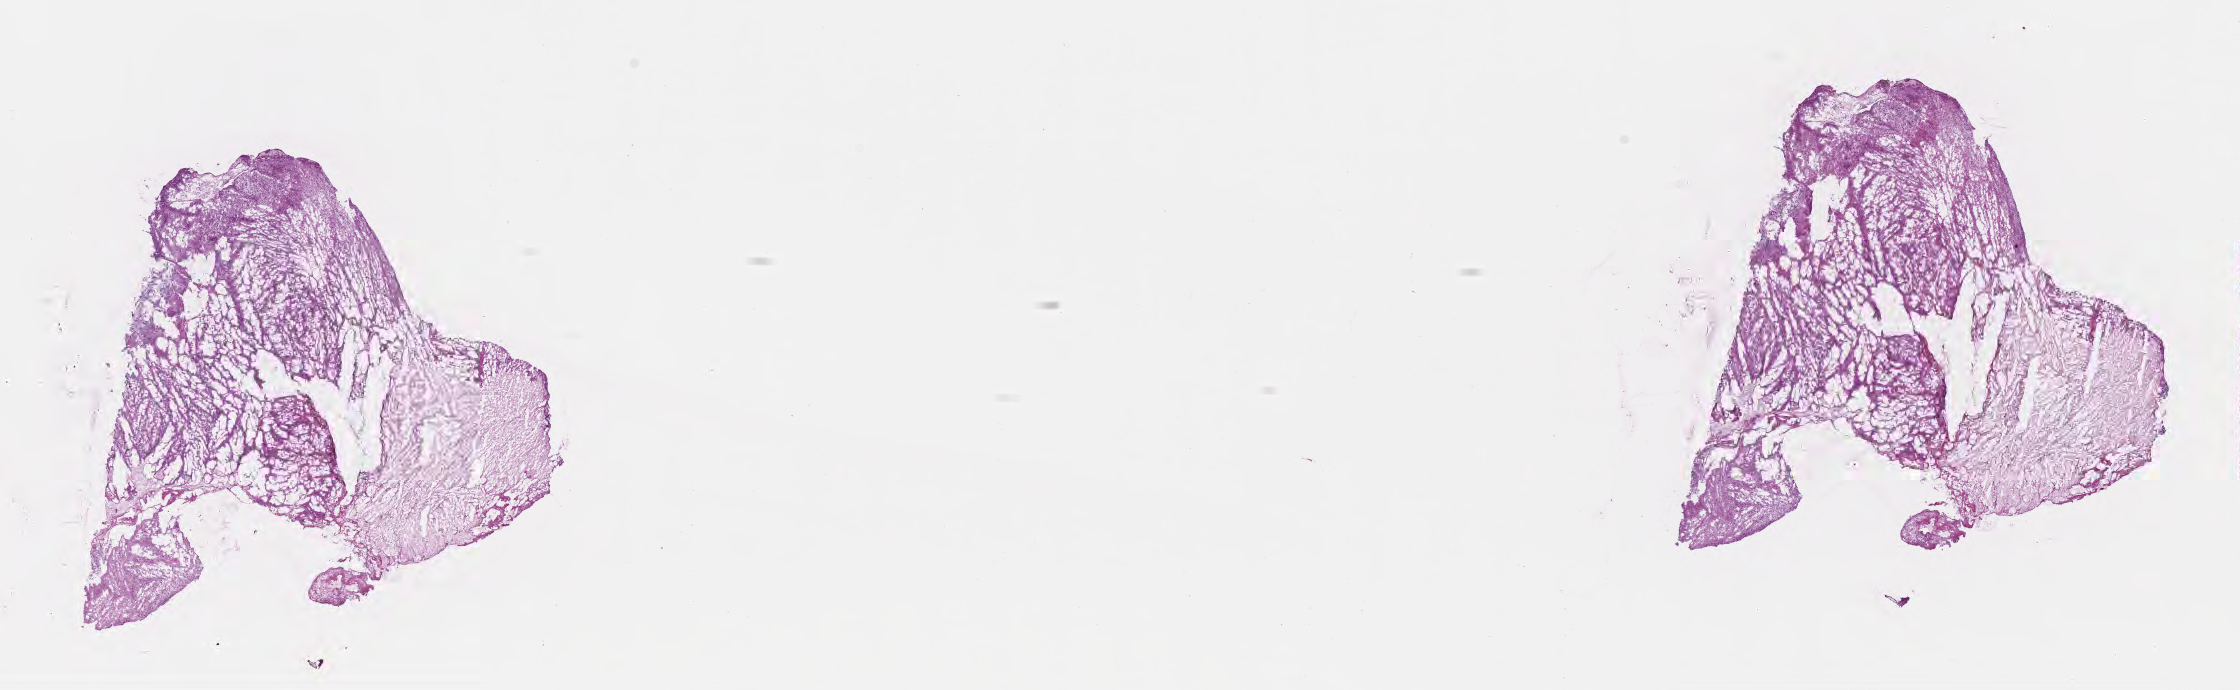
Hematoxylin and eosin (H&E) whole-slide image — low-resolution overview of the scanned area, about 18.1 x 5.6 mm; frozen section; primary tumor; anatomic site: brain. Male, age 75 years at initial diagnosis. Slide review estimates, as recorded: tumor cells 17%, tumor nuclei 94%, stromal cells 2%, necrosis 80%, normal cells 1%. Inflammatory infiltration, as recorded: lymphocyte infiltration 0%, monocyte infiltration 0%, neutrophil infiltration 0%.
Diagnosis: Glioblastoma, NOS. Section: bottom of the tissue portion.